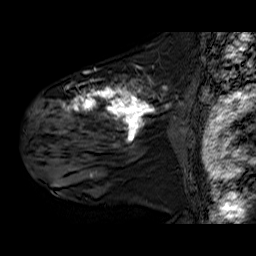
Breast MRI (dynamic contrast-enhanced), one sagittal slice. Position 42 of 60 along the scan axis. Dynamic contrast-enhanced series, time point 2 of 6 at this slice position (early post-contrast). 1.5 T. TE 6.3 ms, TR 32.9 ms. 4 mm slice thickness. 256 × 256 image matrix, field of view 200 × 200 mm. Female patient. Case-level facts recorded for this patient, not image findings: setting: breast cancer imaged before/during neoadjuvant chemotherapy; receptor status: HER2-positive.
Outlined on this slice (semi-automatic segmentation, software-assisted and operator-edited):
- analysis volume of interest (the breast-tissue region the enhancement analysis was run in; not a lesion): bounding box (x1, y1, x2, y2) in pixels: (30, 78, 179, 180)
- tumour enhancement mask (voxels above the 100 % enhancement threshold inside the analysis volume of interest): (62, 79, 171, 178)